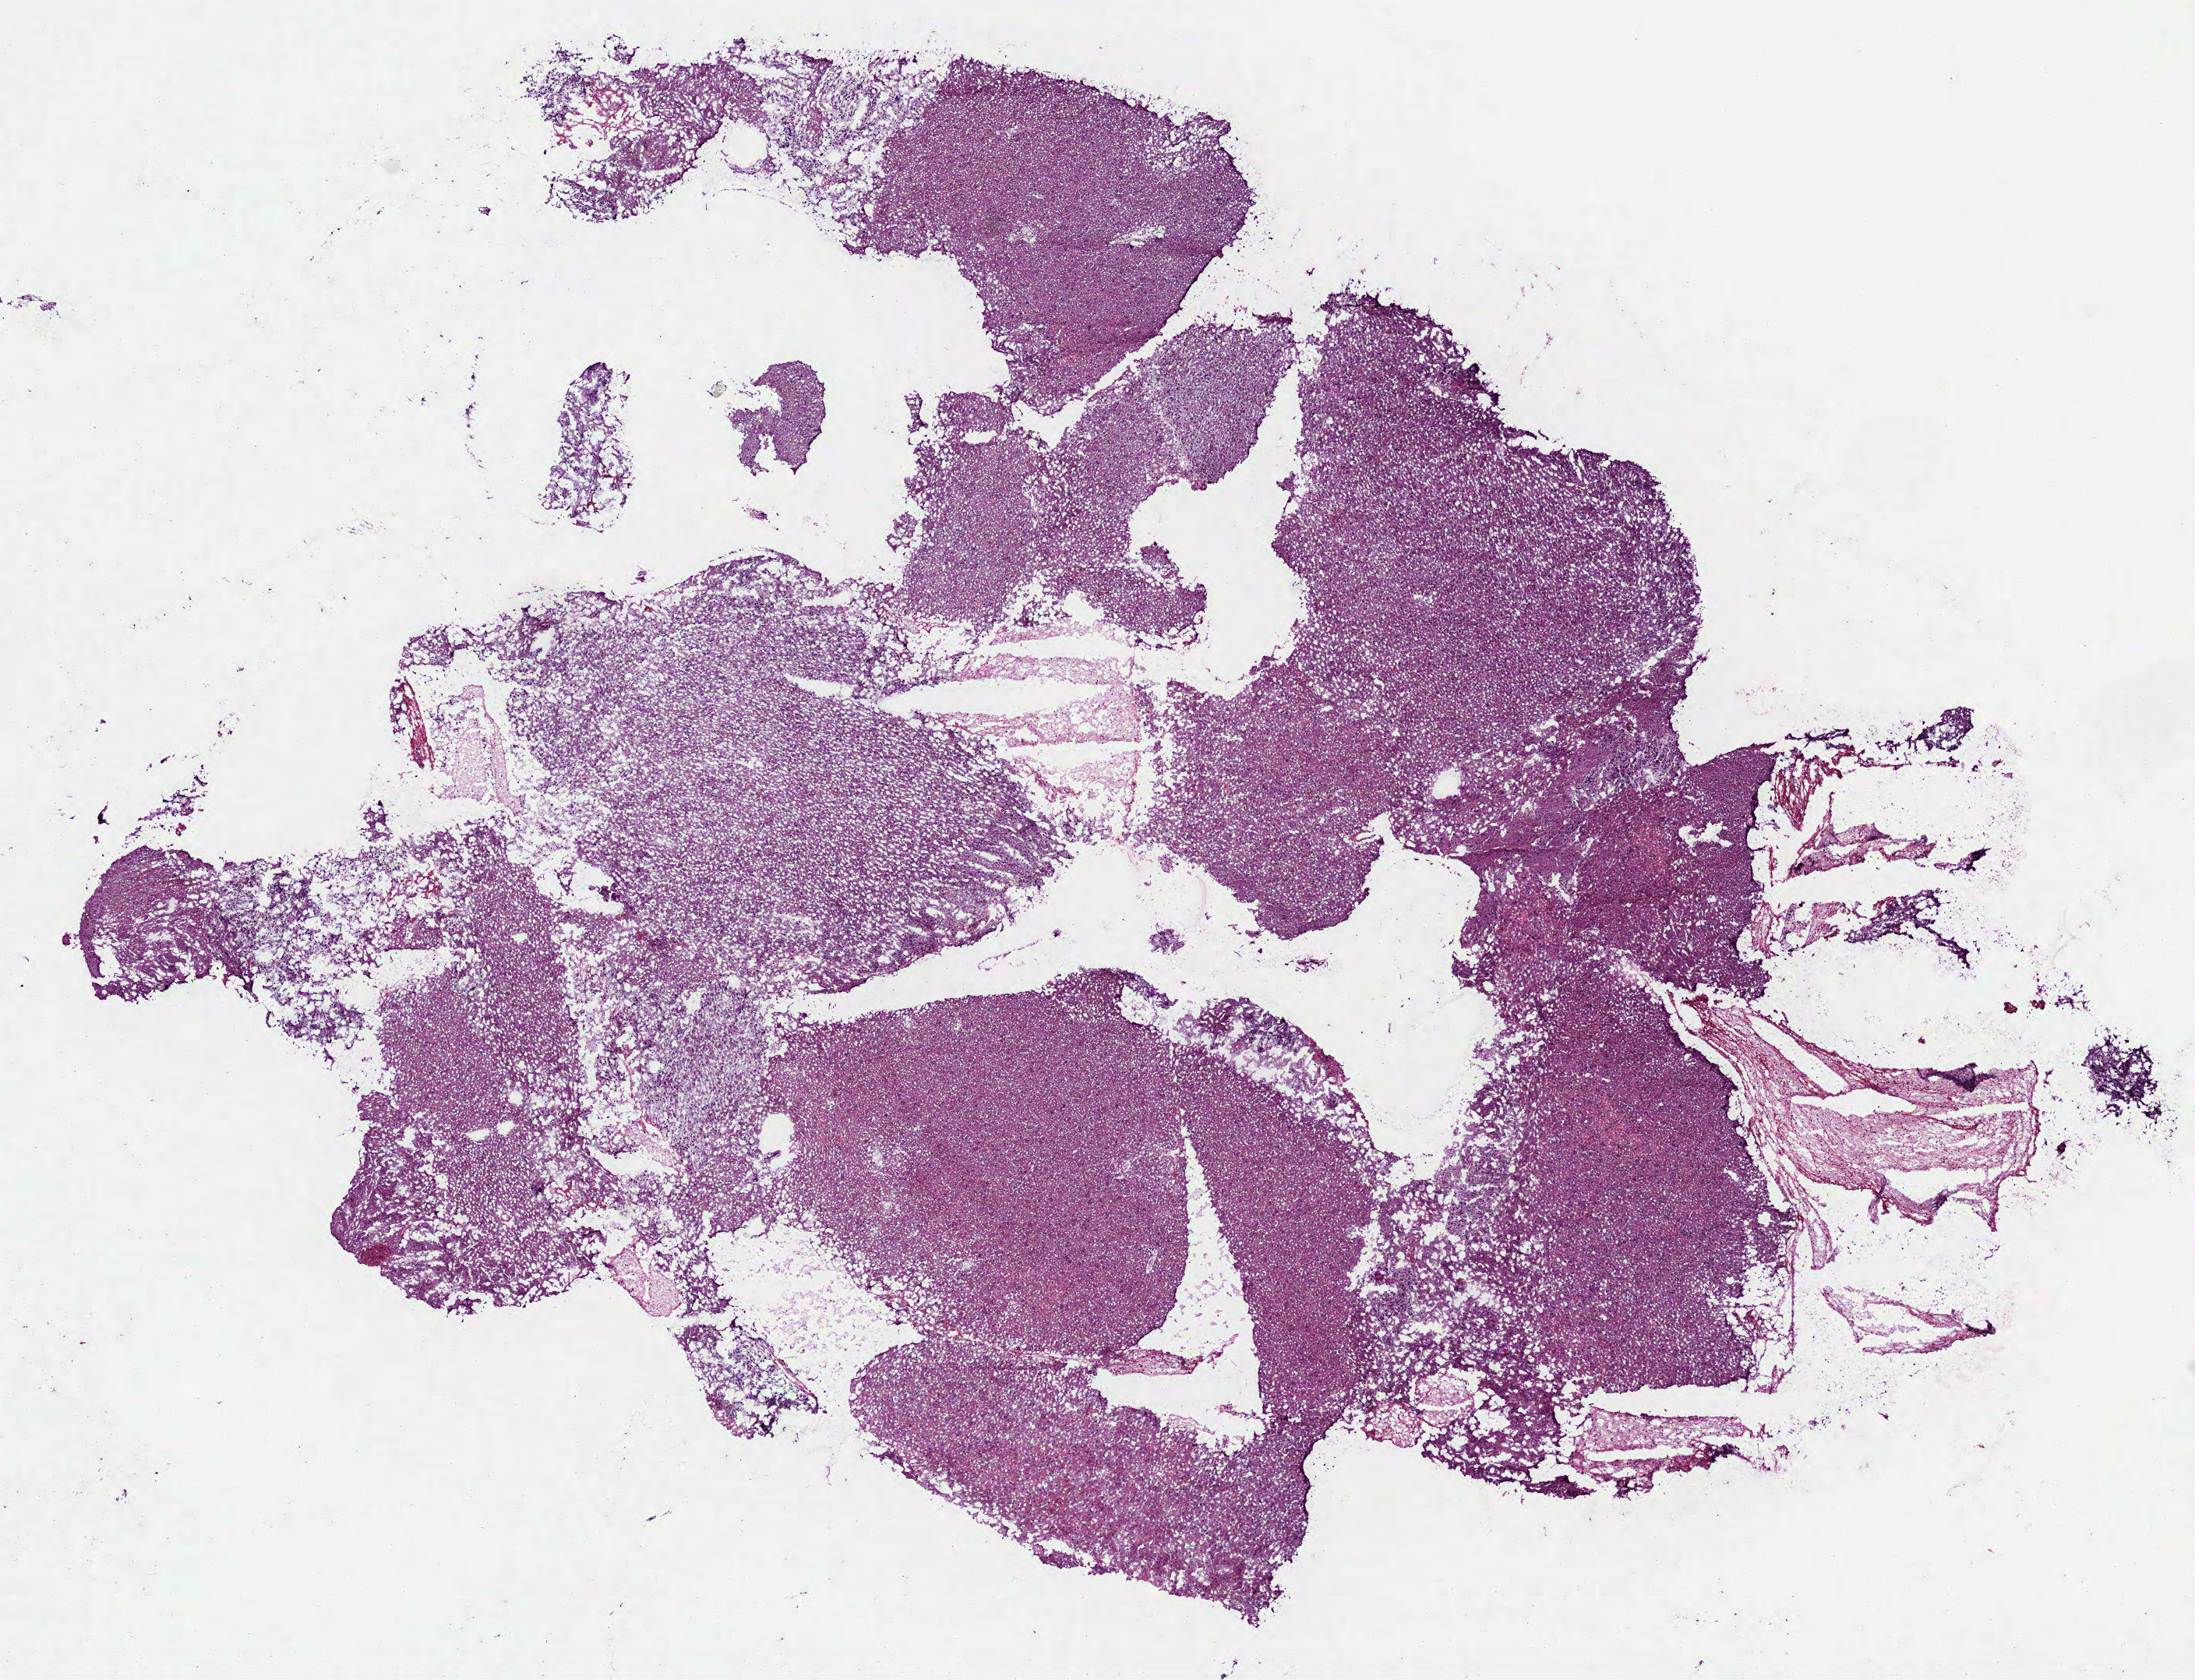
Whole-slide histology image, Hematoxylin and eosin (H&E) stained, shown as a low-resolution overview of the whole scanned area (about 11.4 x 8.7 mm, slide scanned at 40x); frozen section from the top of the tissue portion; sample: primary tumour, brain. Patient: male, age at initial diagnosis 67 years. Histologic grade: G3 (poorly differentiated). Pathologist review of this section (percent, as recorded): tumour cells 75%, tumour nuclei 60%, normal cells 25%, stromal cells 0%, necrosis 0%.
Pathologic diagnosis: Mixed glioma.